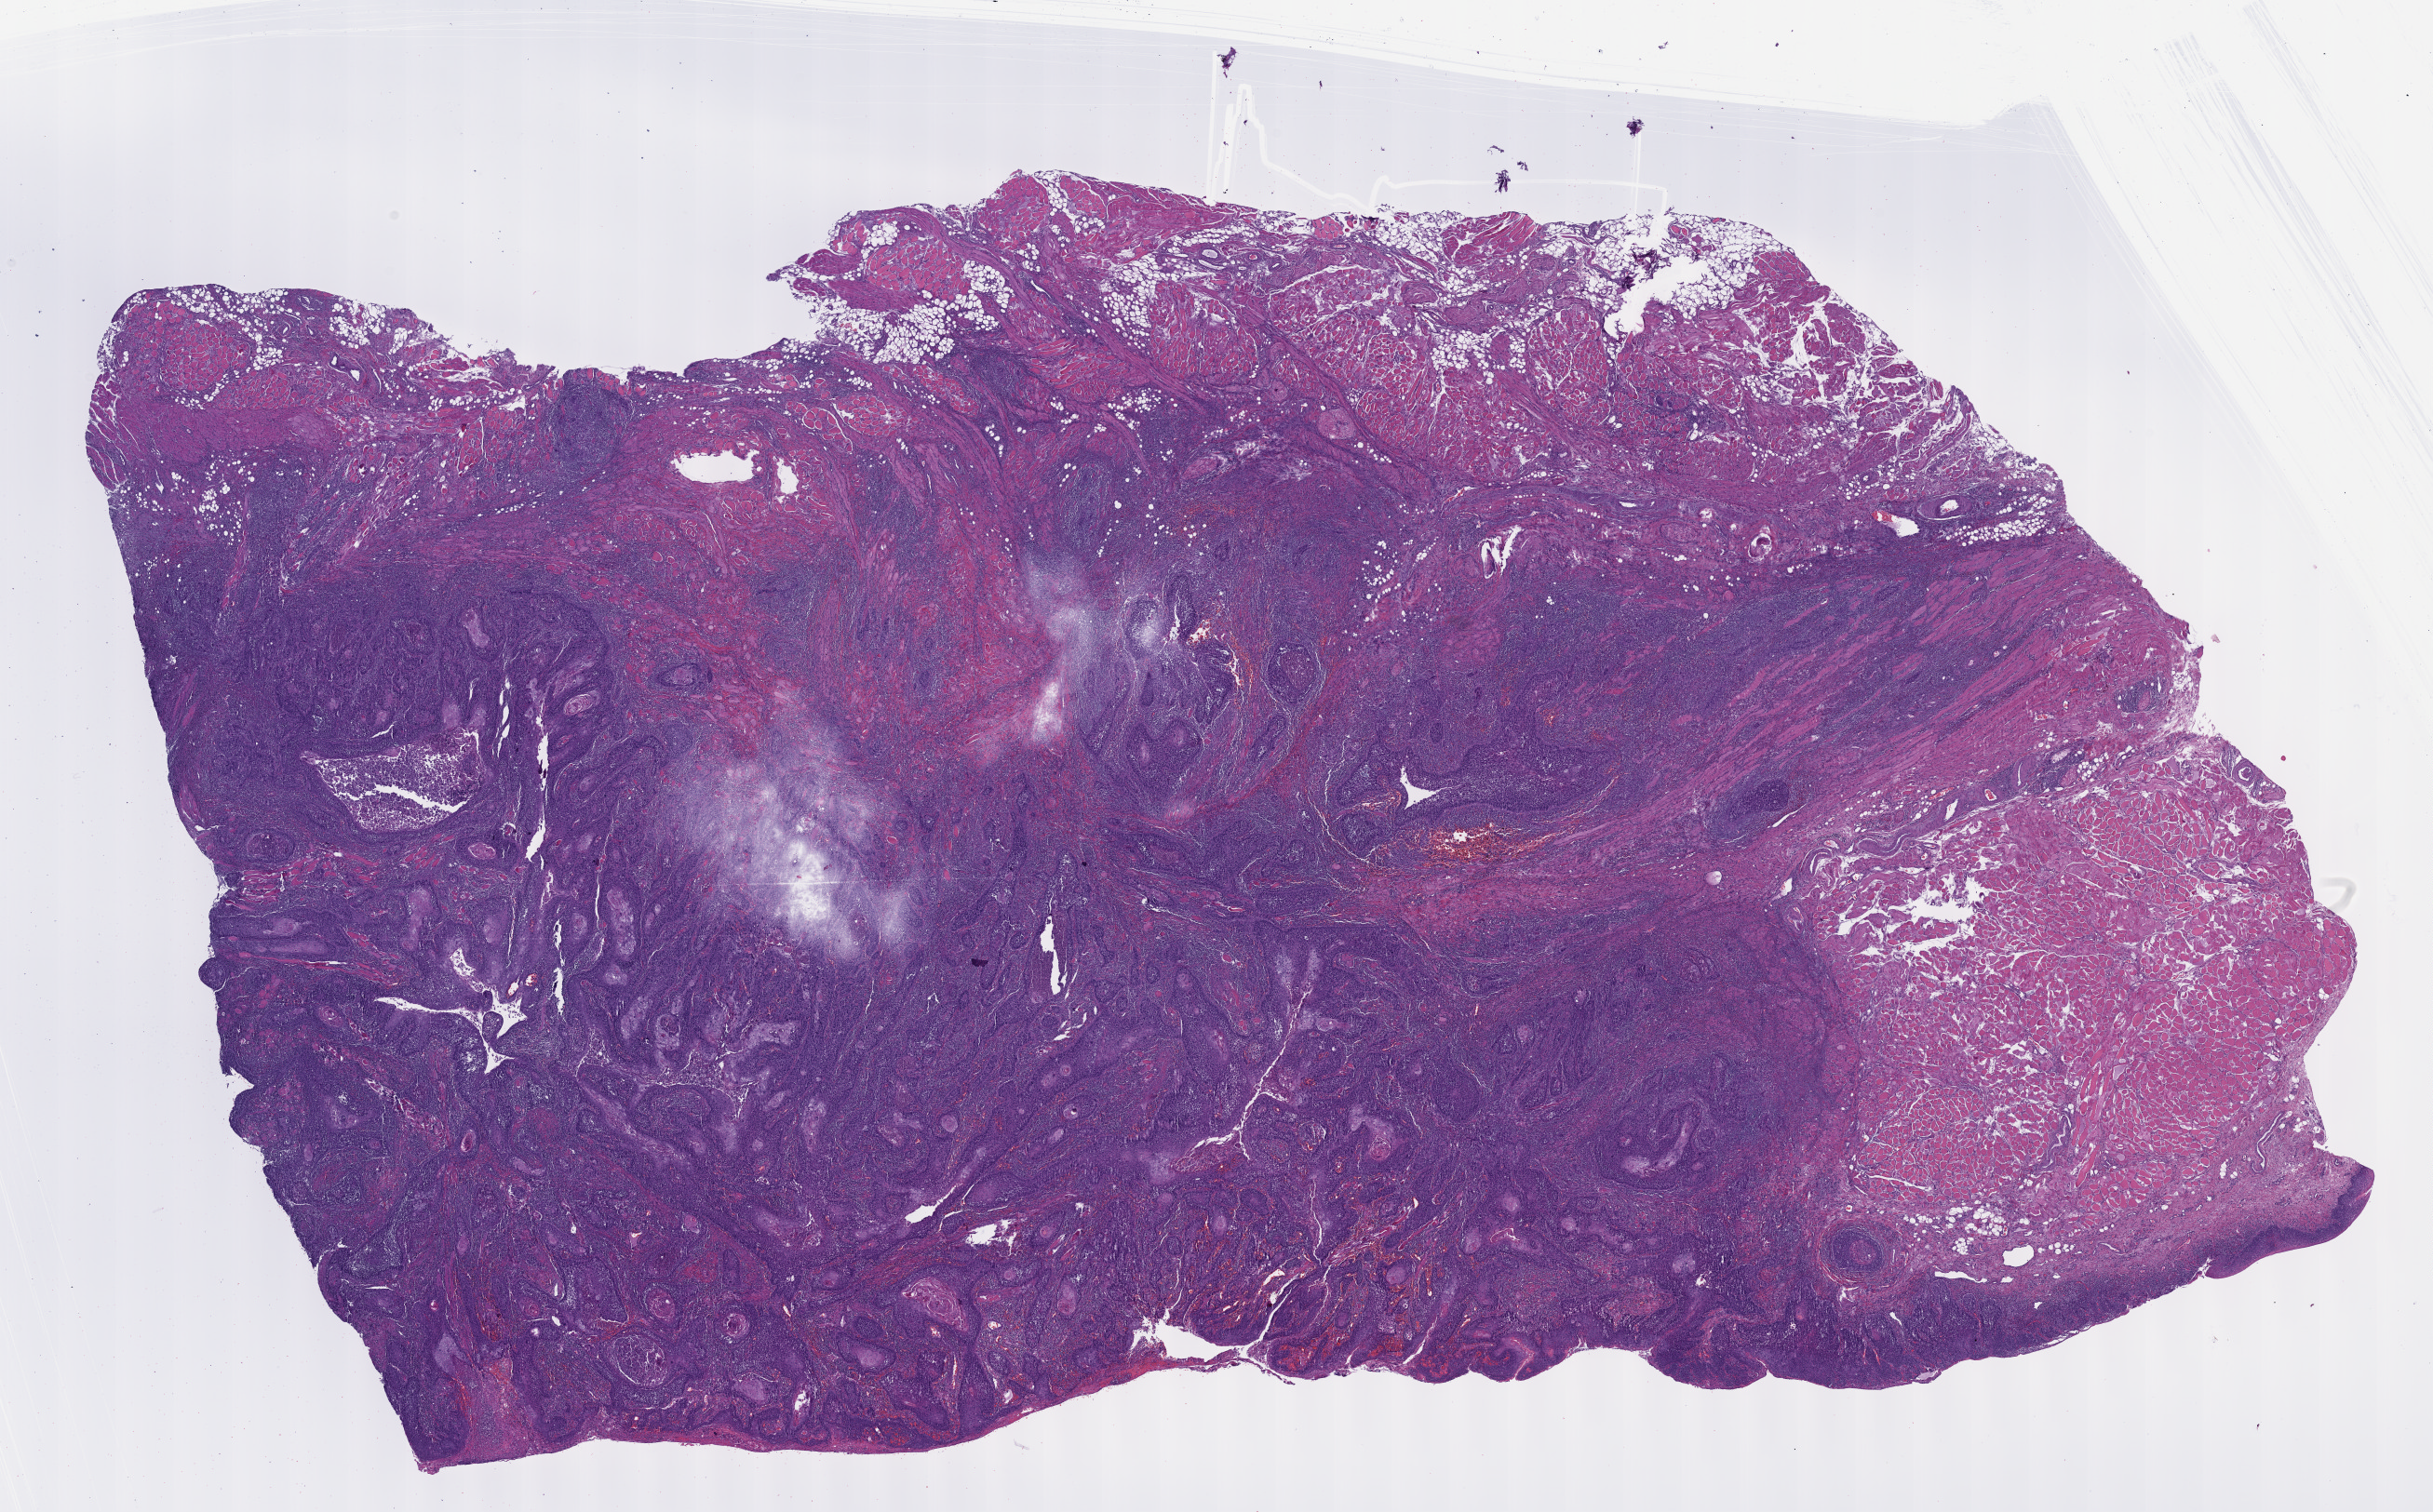
Digitized H&E-stained tissue section (whole slide), a low-resolution overview of the entire scanned area, about 21.1 x 13.1 mm (from a 40x scan), formalin-fixed paraffin-embedded (FFPE) diagnostic section, sample: primary tumour, head and neck. Male patient; age at initial diagnosis 60 years. Histologic grade: G2 (moderately differentiated).
Laterality: right. Histologic diagnosis: Squamous cell carcinoma, NOS (tongue, NOS). AJCC pathologic stage: IVA.